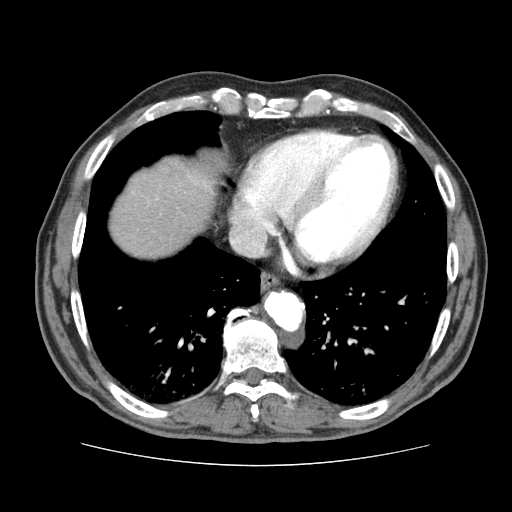
Contrast-enhanced abdominal CT (liver protocol), one axial slice; slice 73 of 79 in the series (ordered by position); reconstruction kernel STANDARD; 120 kVp; soft-tissue window (W 400 / L 40 HU); 512 × 512 image matrix, field of view 360 × 360 mm. From the clinical record (not read from this slice): diagnosis: hepatocellular carcinoma (patient treated with transarterial chemoembolisation; whether this scan precedes or follows treatment is not stated here); TNM stage (as recorded): Stage-I; Child-Pugh class: A; tumour nodularity: uninodular.
Structures marked on this image (semi-automatically segmented with operator editing):
- abdominal aorta: bounding box (x1, y1, x2, y2) in pixels: (267, 293, 303, 329)
- liver parenchyma outside the tumour (the mass and vessels are separate outlines, so this box may not span the whole liver): (112, 158, 218, 256)